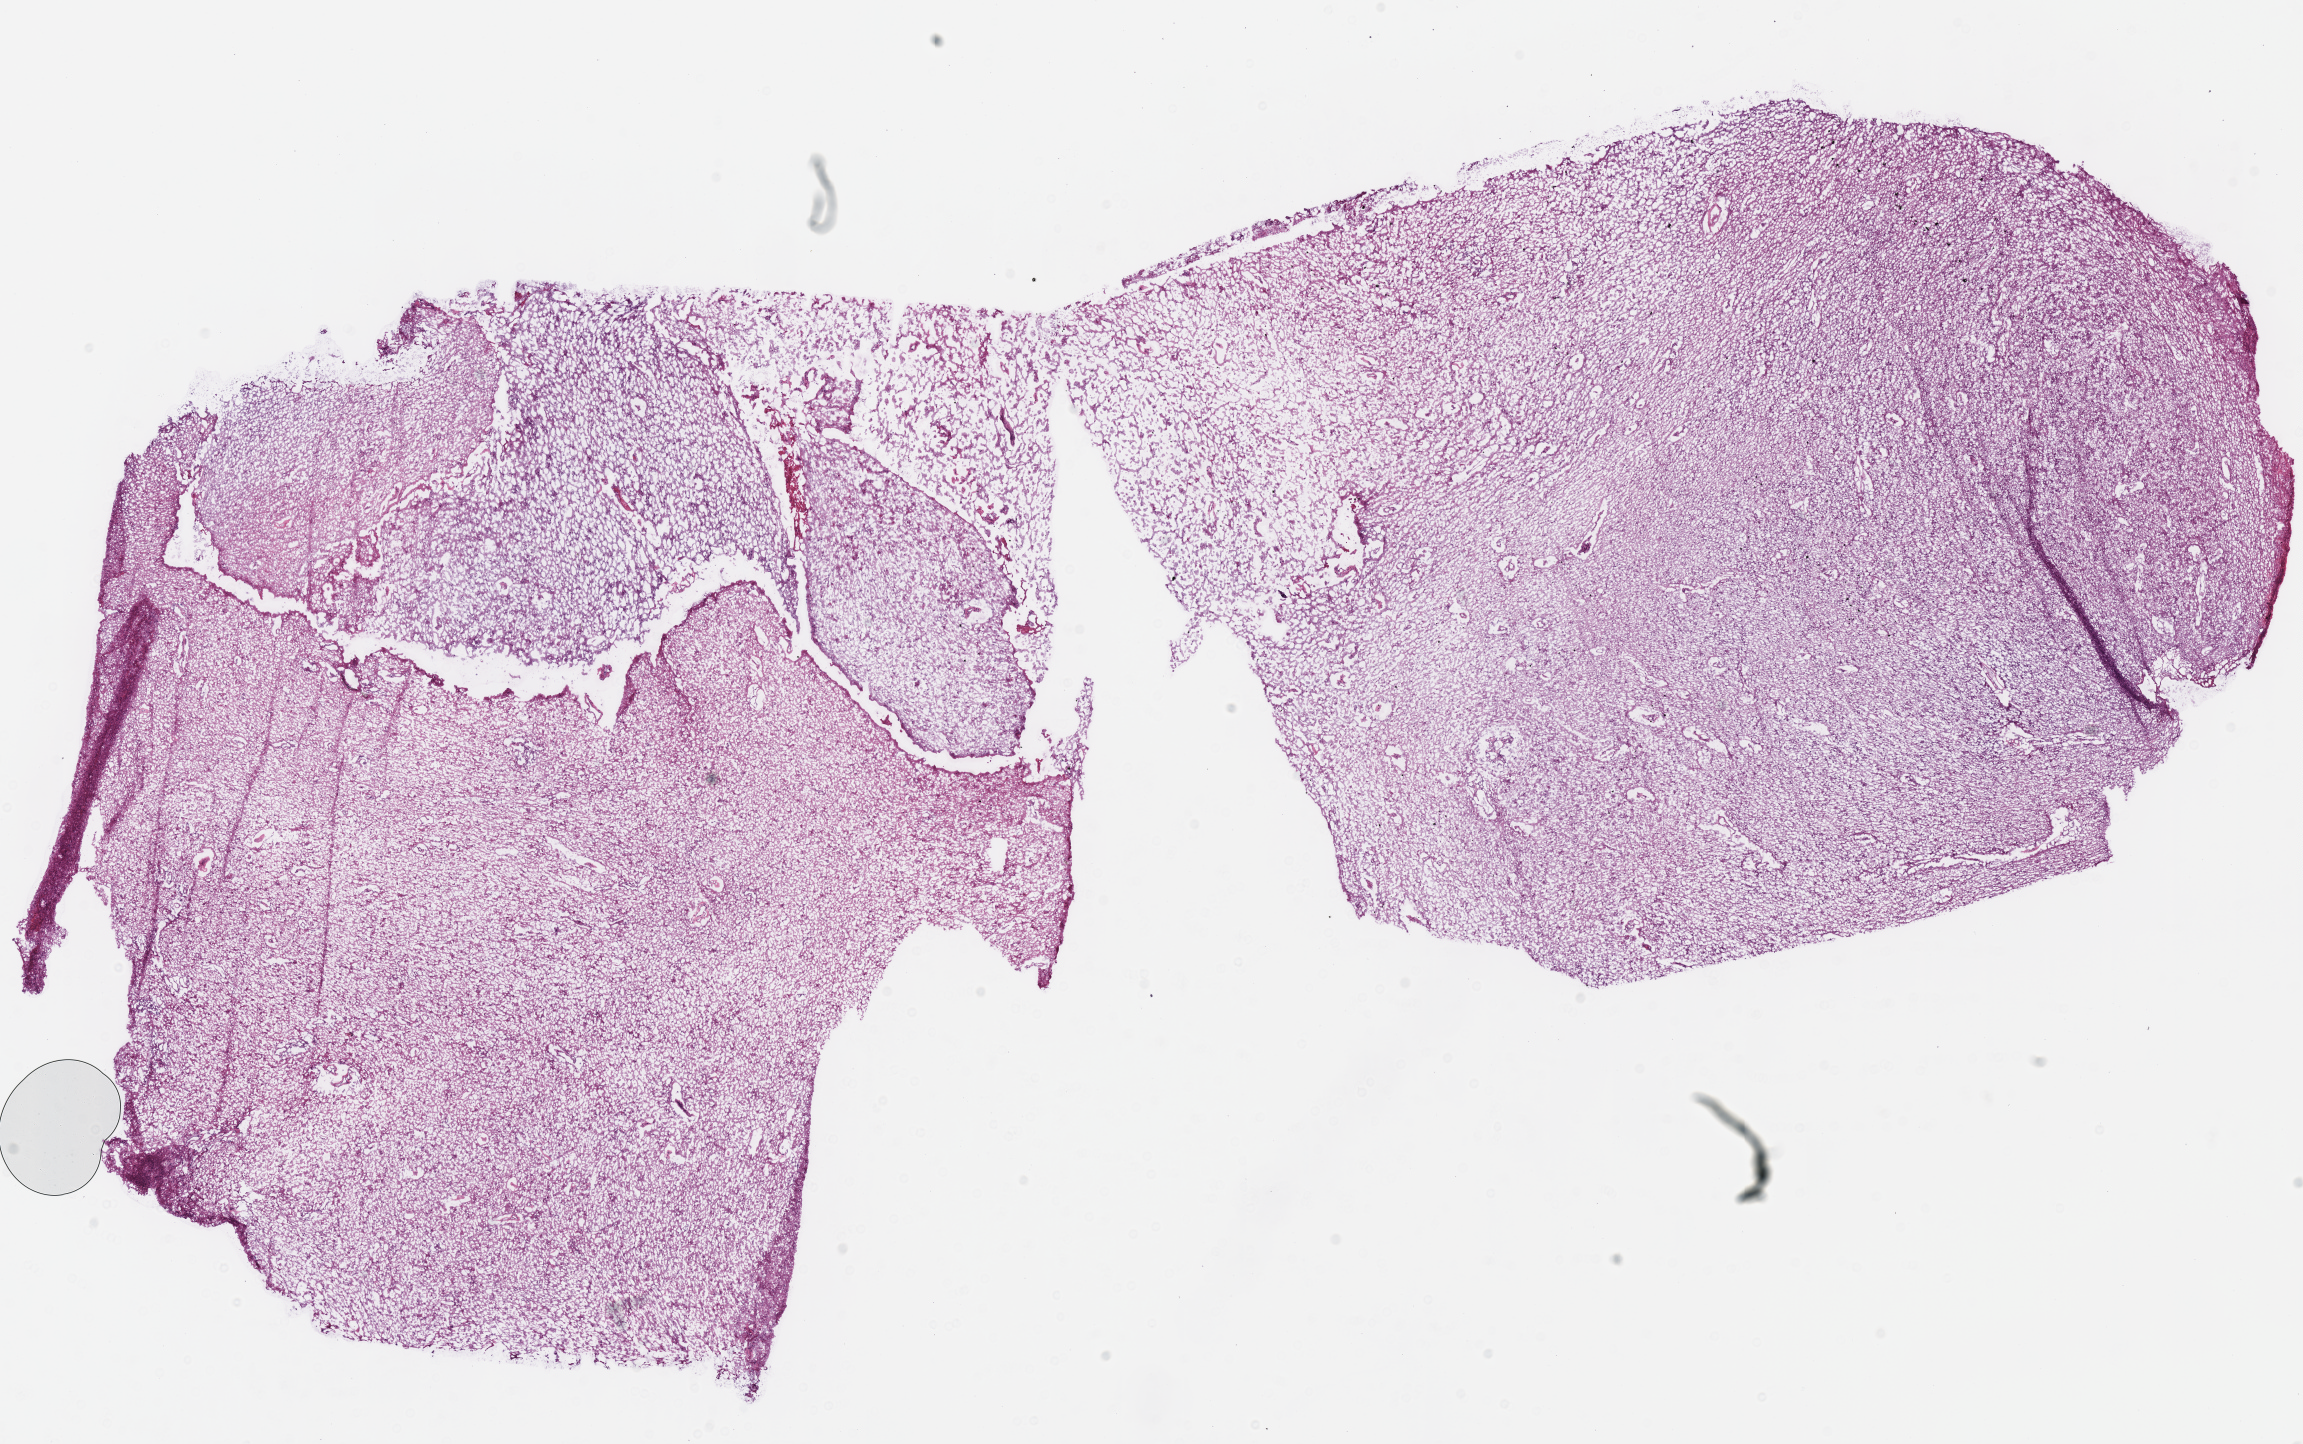
H&E-stained whole-slide image, a low-resolution overview of the entire scanned area, about 18.1 x 11.4 mm; frozen section from the bottom of the tissue portion; primary tumour sample from the brain. Male, age 58 years at initial diagnosis. Histologic grade: G3 (poorly differentiated). Slide review estimates, as recorded: tumour cells 100%, tumour nuclei 65%, normal cells 0%, stromal cells 0%, necrosis 0%.
Diagnosis: Mixed glioma (cerebrum).